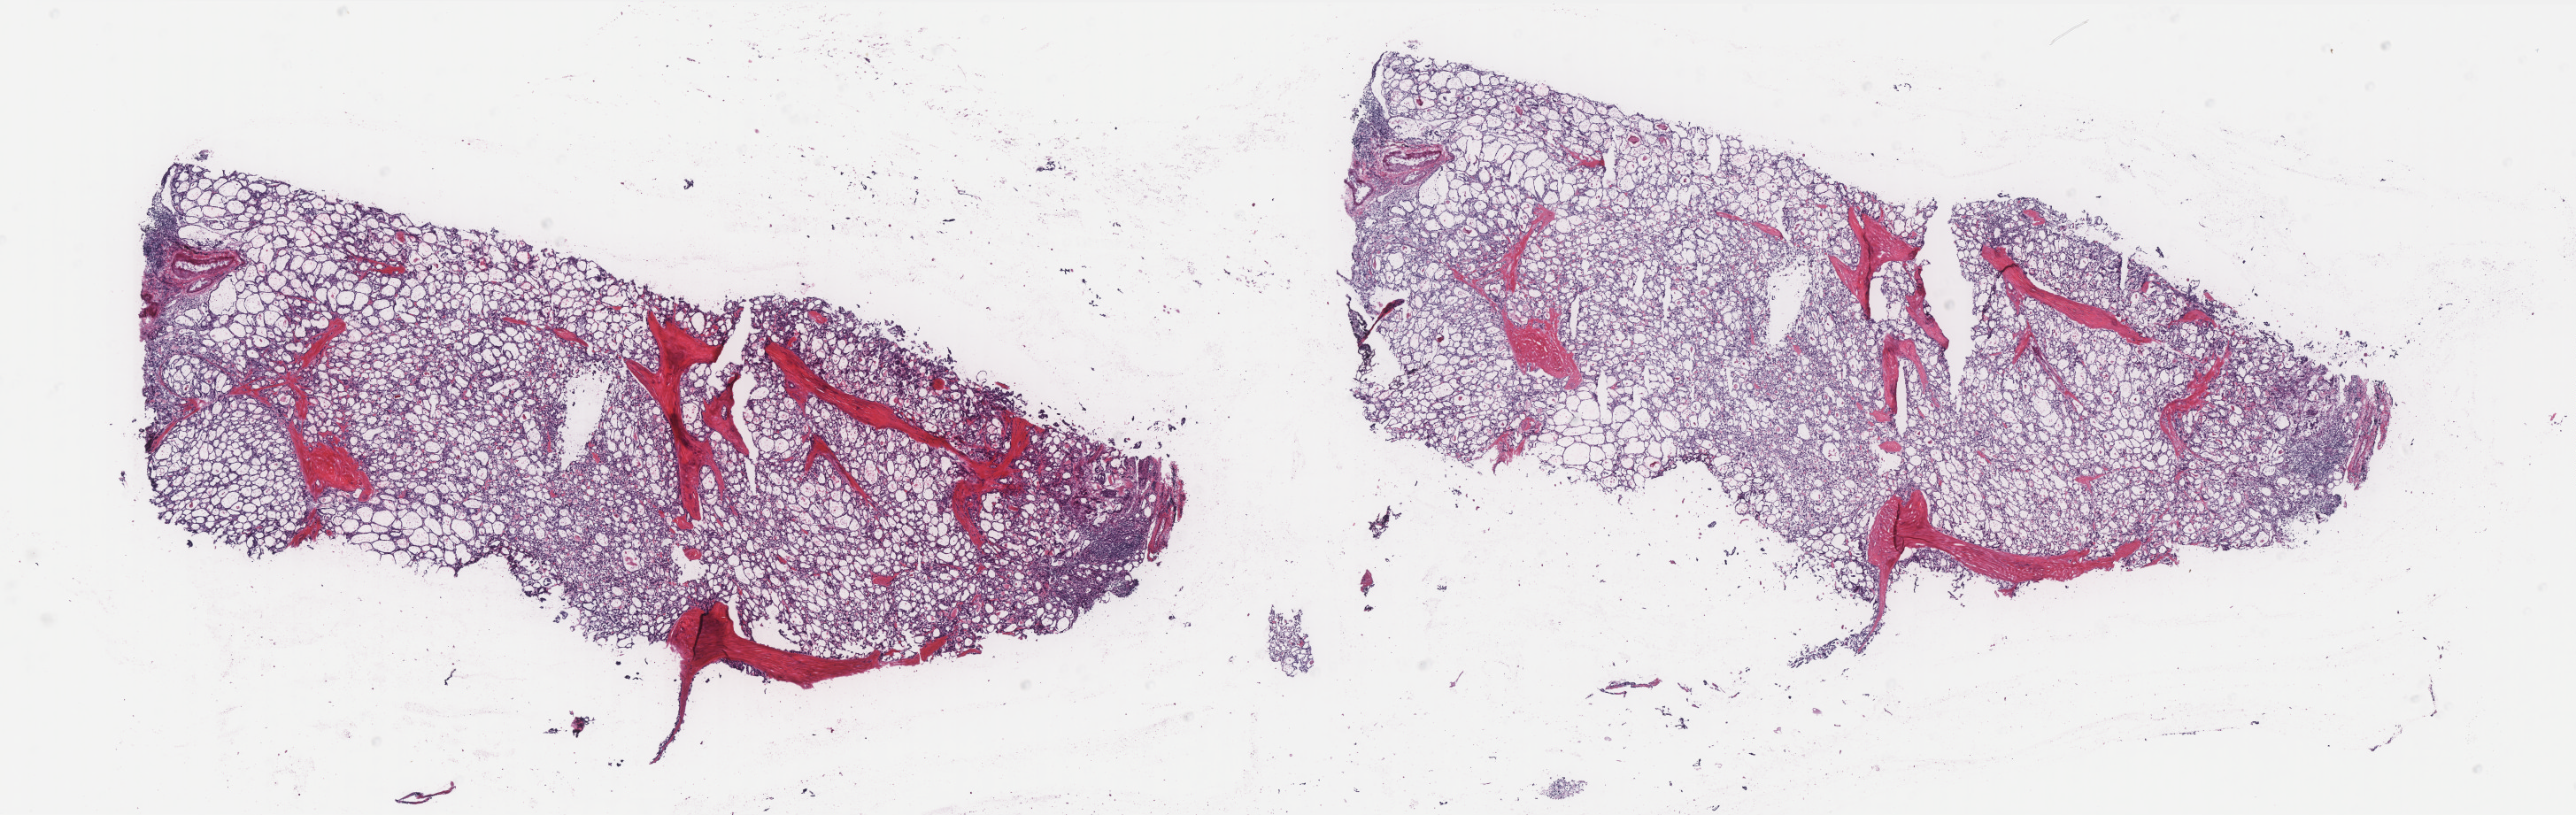
Hematoxylin and eosin (H&E) stained whole-slide image, a low-resolution overview of the entire scanned area, about 23.3 x 7.4 mm (from a 40x scan), frozen section from the top of the tissue portion, thyroid, primary tumour sample. Female, age 33 years at initial diagnosis. Pathologist review of this section (percent, as recorded): tumour cells 0%, tumour nuclei 0%.
Diagnosis: Papillary adenocarcinoma, NOS (thyroid gland).